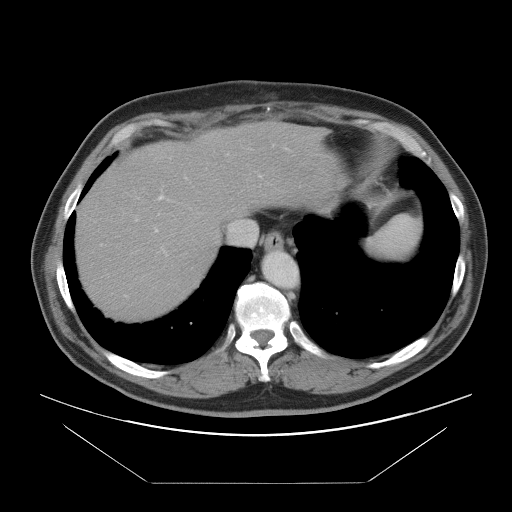
Contrast-enhanced abdominal CT, one axial slice. Slice 78 of 97 in the series (ordered by position). 120 kVp. Intravenous contrast given. Soft-tissue window (W 400 / L 40 HU). 512 × 512 image matrix, field of view 442 × 442 mm. Male patient, age 62 years. Case-level facts recorded for this patient, not image findings: diagnosis: colorectal cancer liver metastases, imaged before liver resection; multiple liver metastases: no; largest metastasis: 7 cm; disease in both lobes: yes.
Structures marked on this image (outlined manually by an expert reader):
- hepatic veins: bounding box <228,220,256,245> (left, top, right, bottom; pixels)
- liver: <76,124,337,317>
- planned liver remnant (the part of the liver to remain after resection): <76,173,224,317>
- portal vein (with intrahepatic branches): <135,145,288,254>